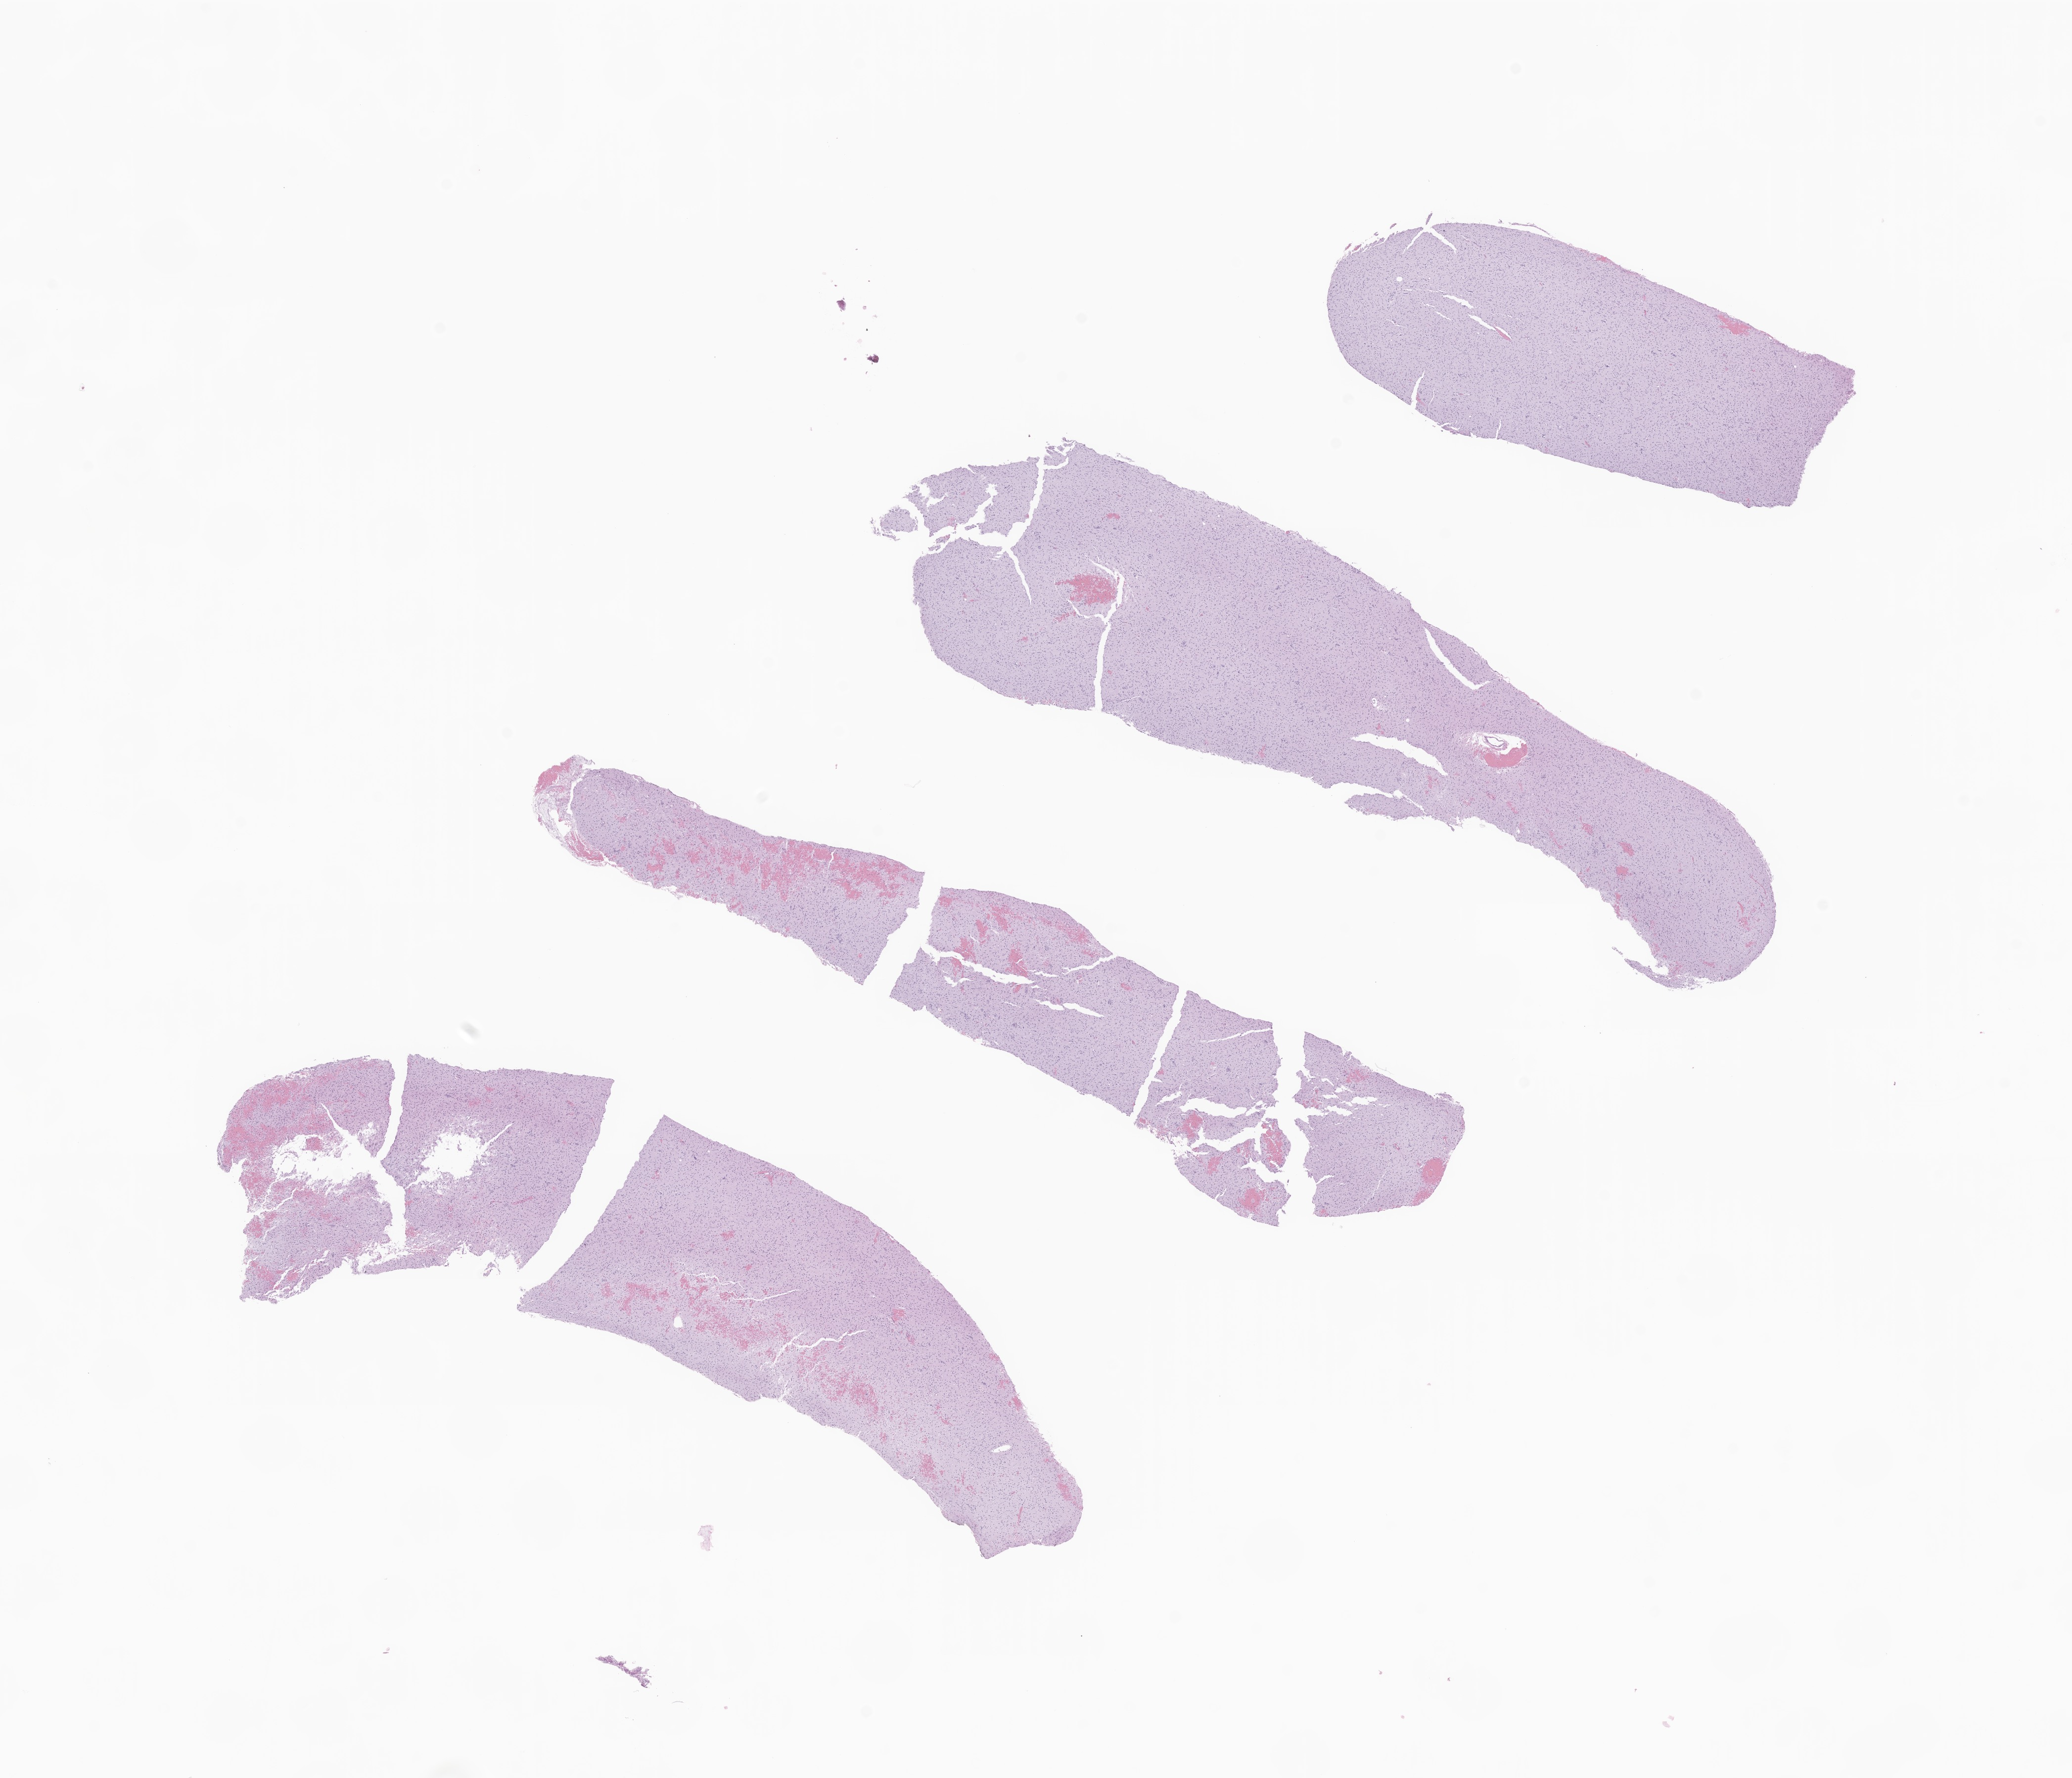
H&E whole-slide image of tumor tissue from the brain, whole scanned area (about 17.7 x 15.2 mm) shown as a low-resolution overview. Formalin-fixed paraffin-embedded section. Patient: female, age 223 months.
Diagnosis (ICD-O-3 morphology term): Glioma, malignant.